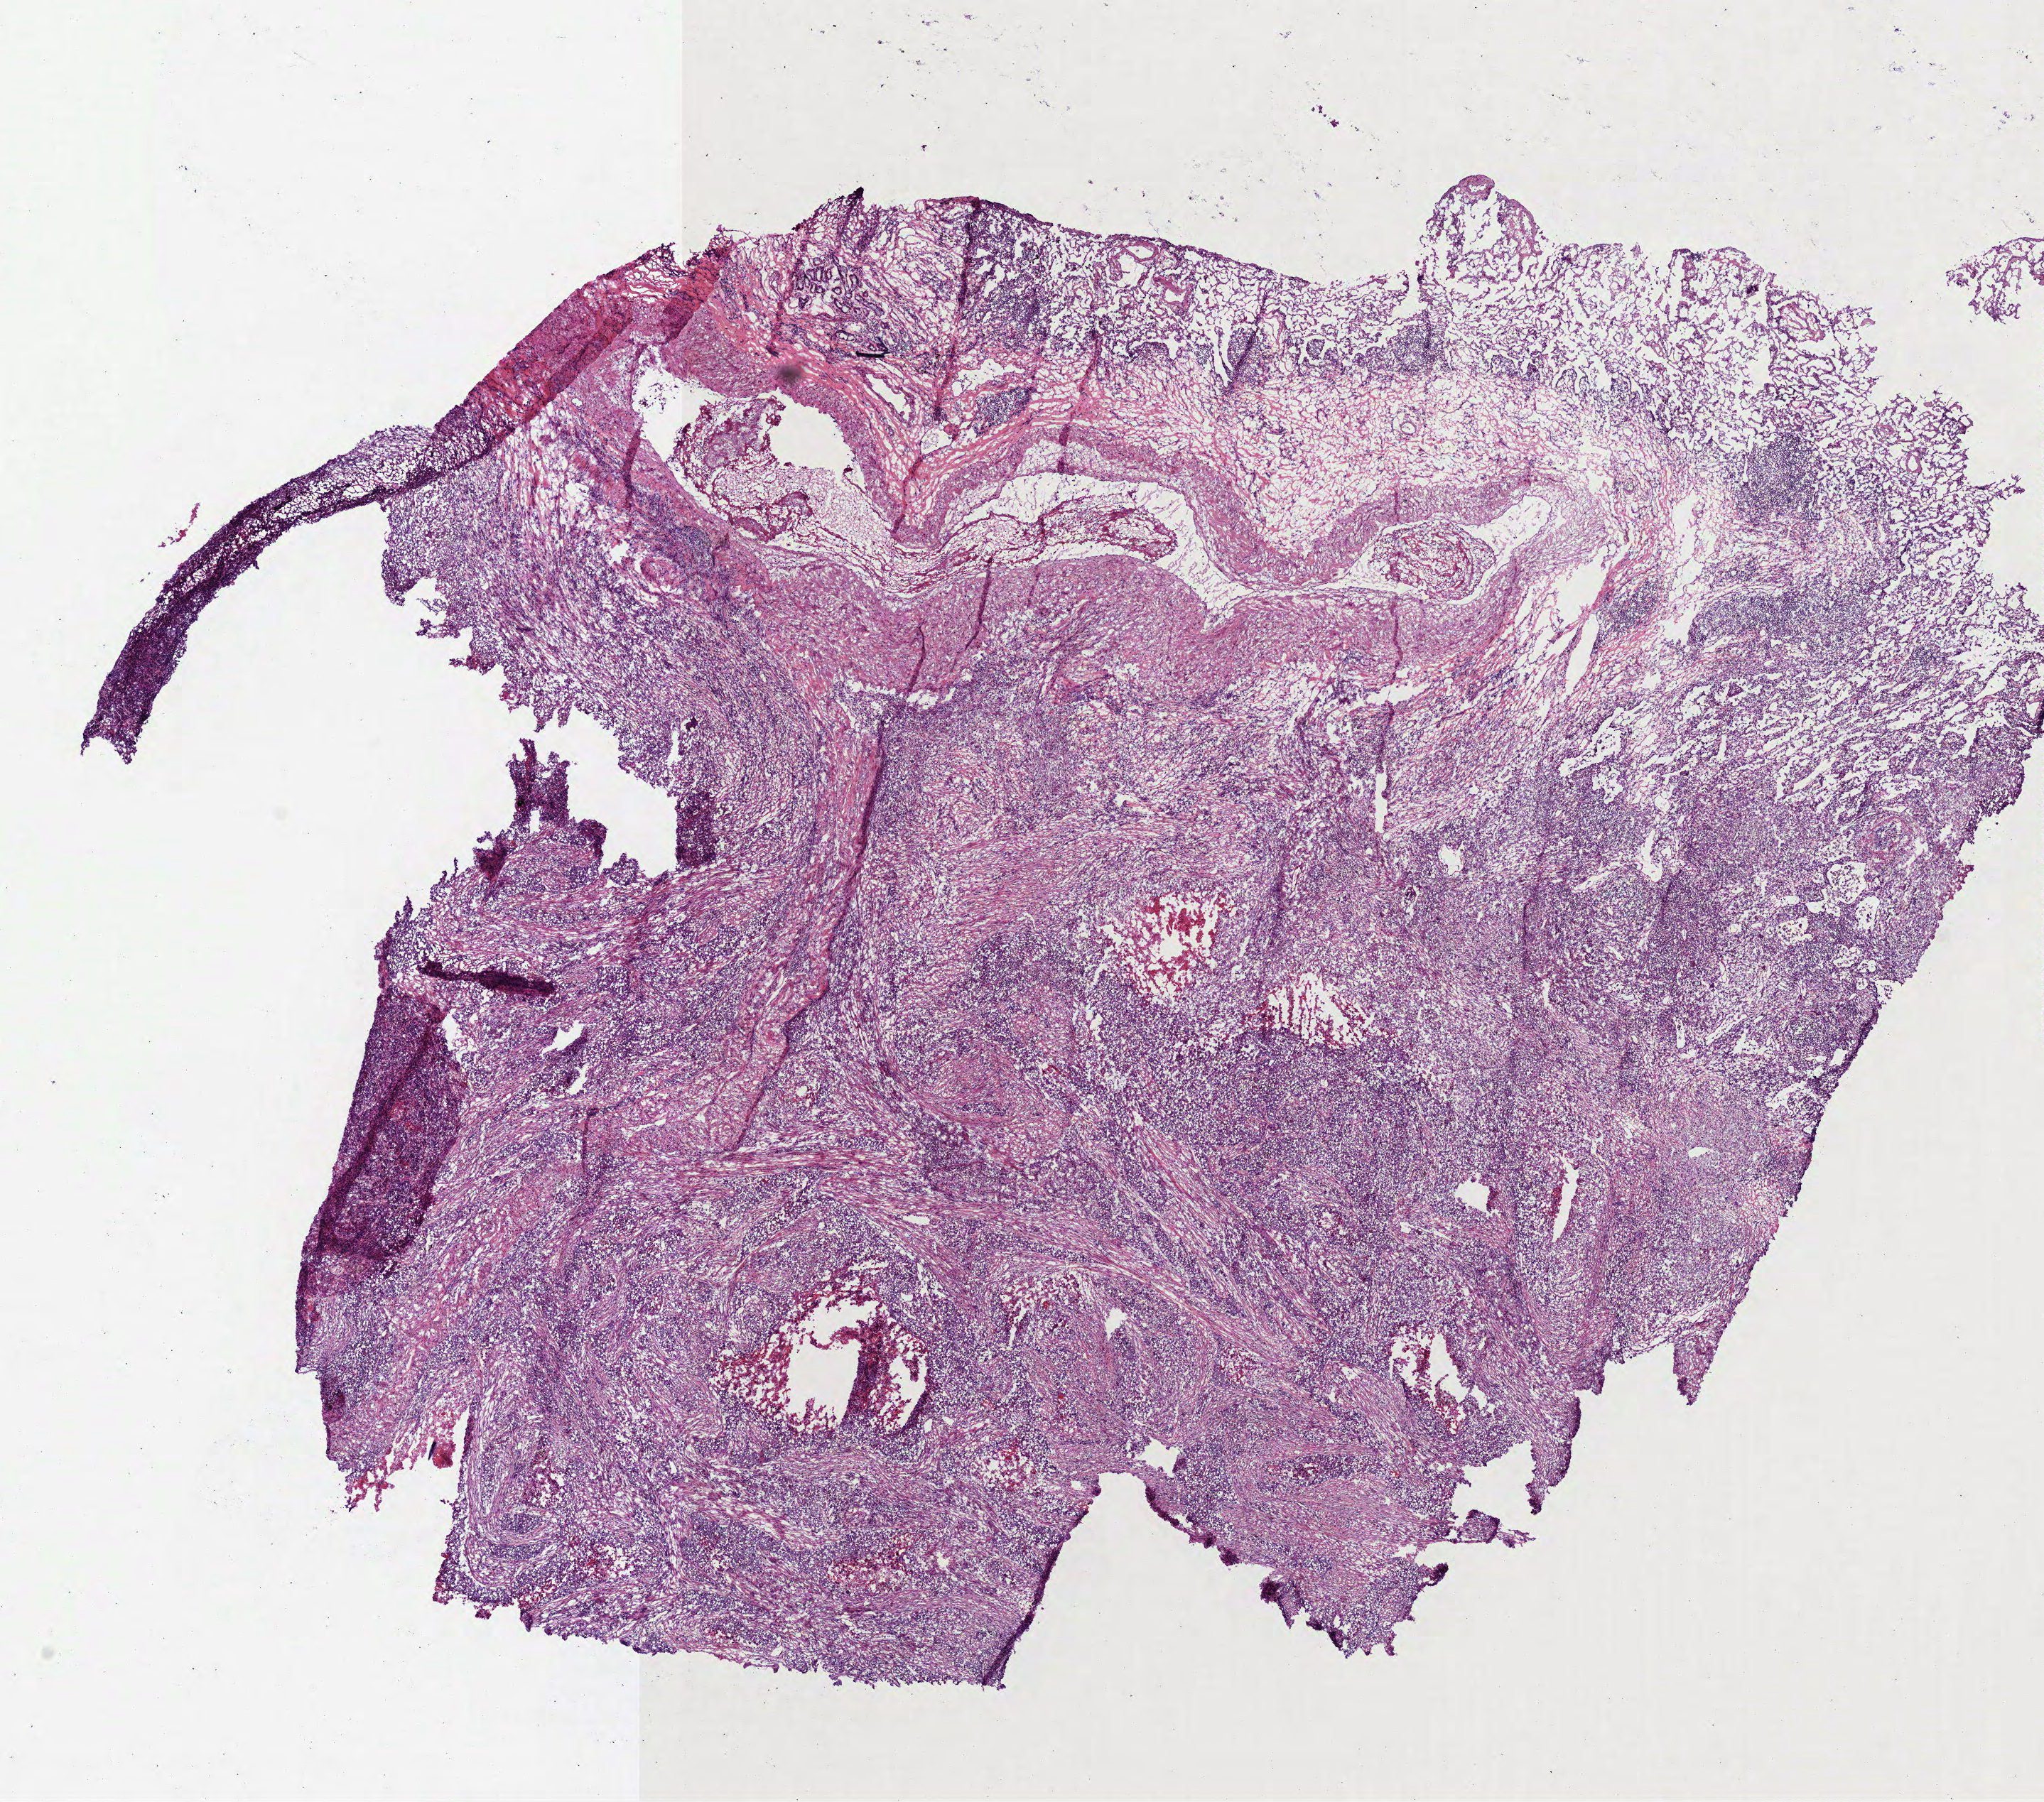
Digitized H&E-stained tissue section (whole slide), low-resolution overview of the scanned area, about 11.6 x 10.2 mm (slide scanned at 40x), frozen section from the top of the tissue portion, primary tumour sample from the lung. Male, age 62 years at initial diagnosis. Slide review estimates, as recorded: tumour cells 70%, tumour nuclei 65%, normal cells 10%, stromal cells 15%, necrosis 5%.
* histologic diagnosis: Squamous cell carcinoma, NOS
* AJCC pathologic stage: IIA (7th edition)
* laterality: left